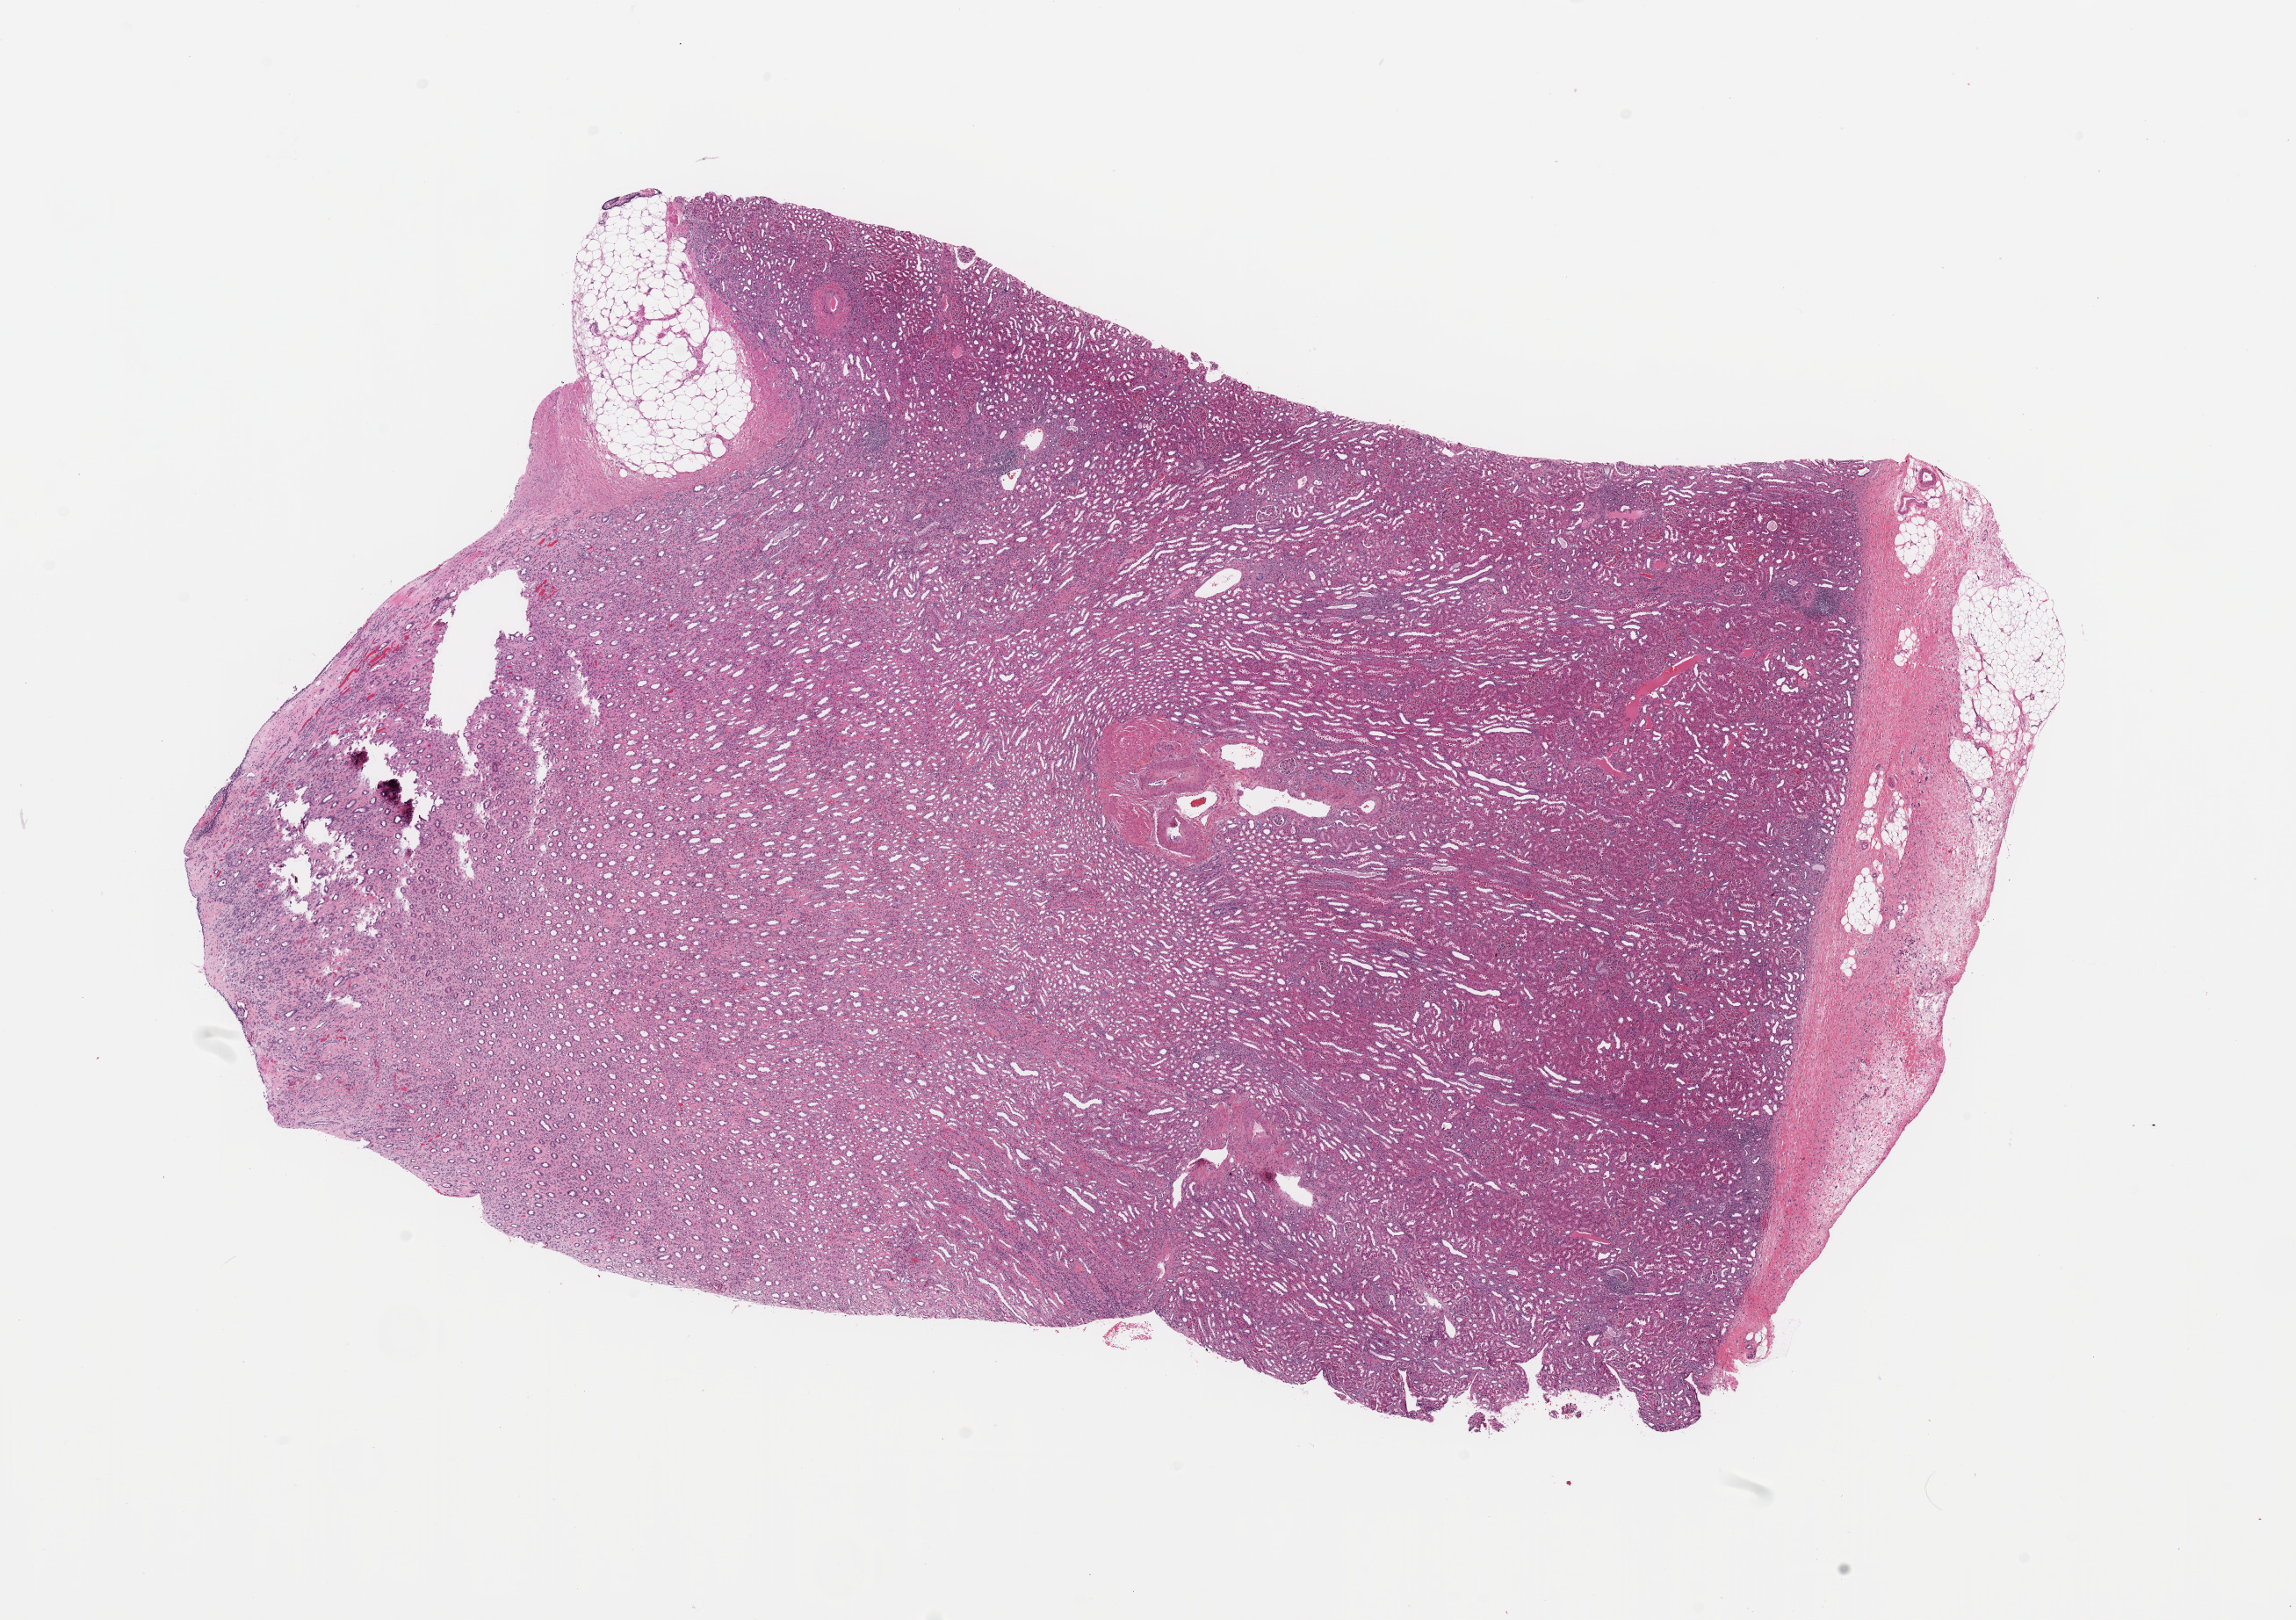
Whole-slide histology image, H&E-stained — low-resolution overview of the scanned area, about 20.7 x 14.6 mm (acquisition: 20x scan); normal (non-tumour) tissue sample, sampled site: kidney. Patient: male, age 40 years.
This section: normal (non-tumour) tissue from the same patient. Patient diagnosis: Renal cell carcinoma, NOS.